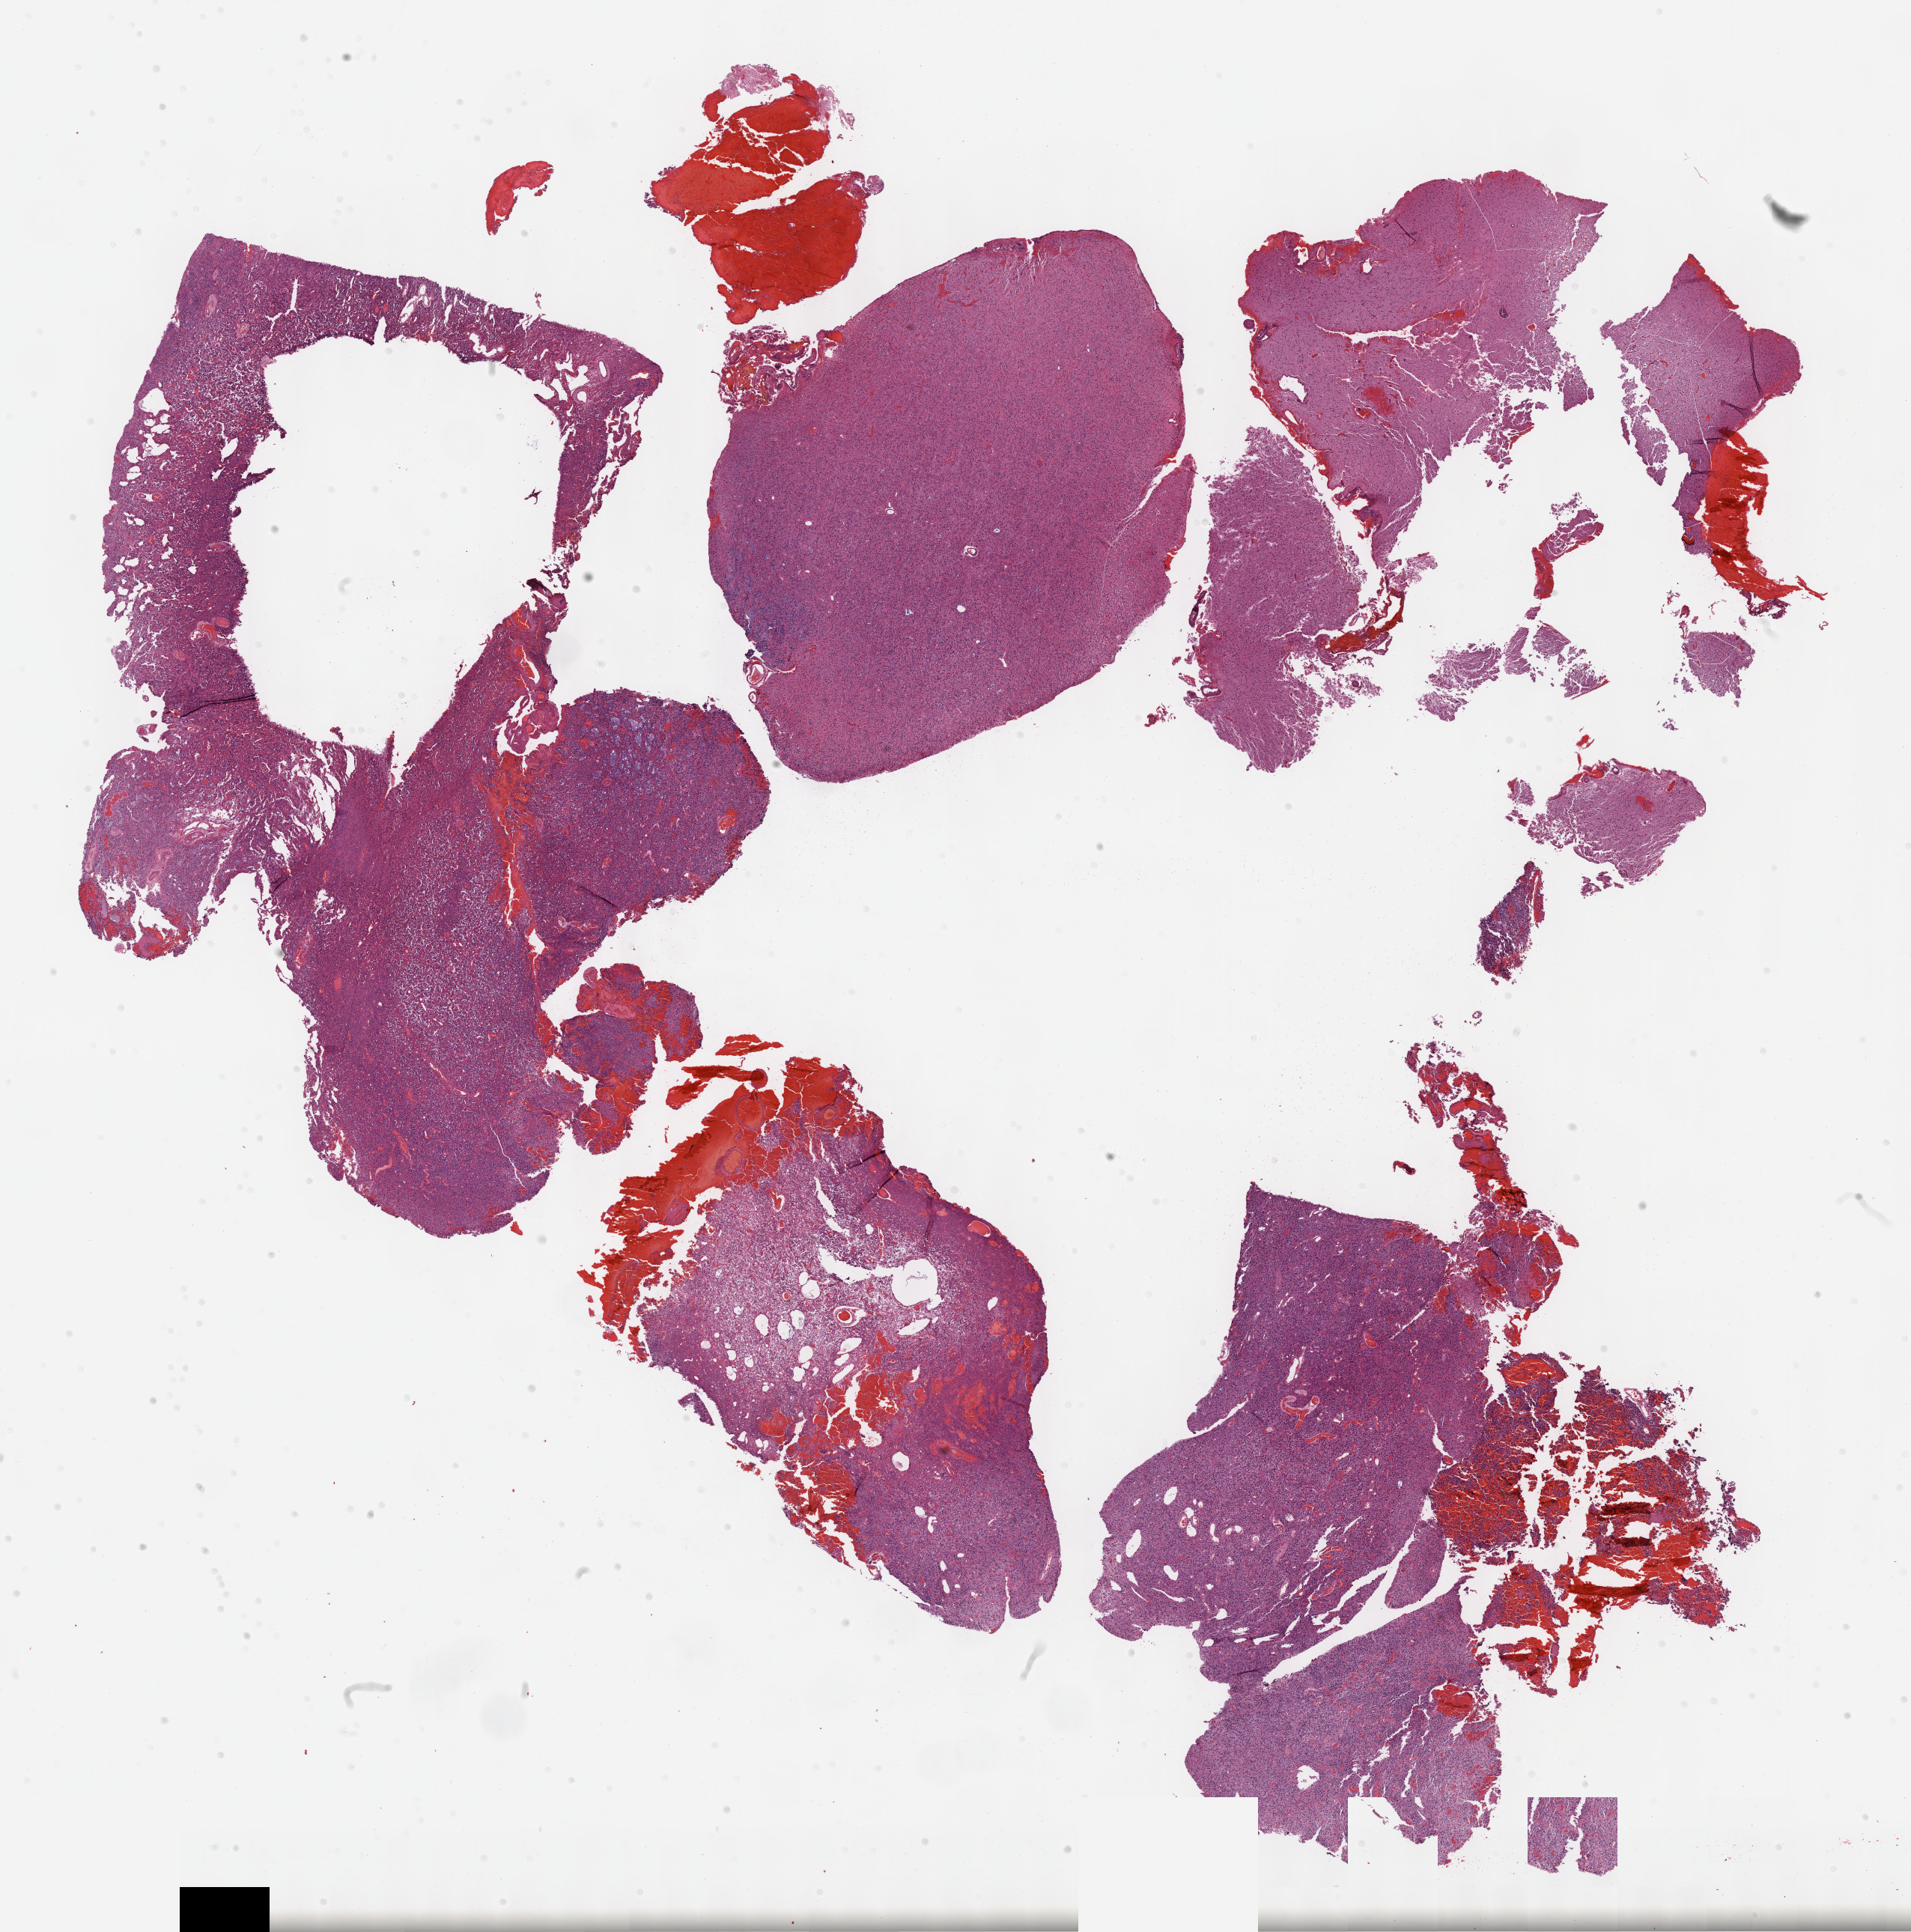
H&E whole-slide image, shown as a low-resolution overview of the whole scanned area (about 20.6 x 20.9 mm, slide scanned at 40x), FFPE section, primary tumour sample from the brain. Male, age 39 years at initial diagnosis. Histologic grade: G3 (poorly differentiated).
Laterality: left. Histologic diagnosis: Astrocytoma, anaplastic (cerebrum).